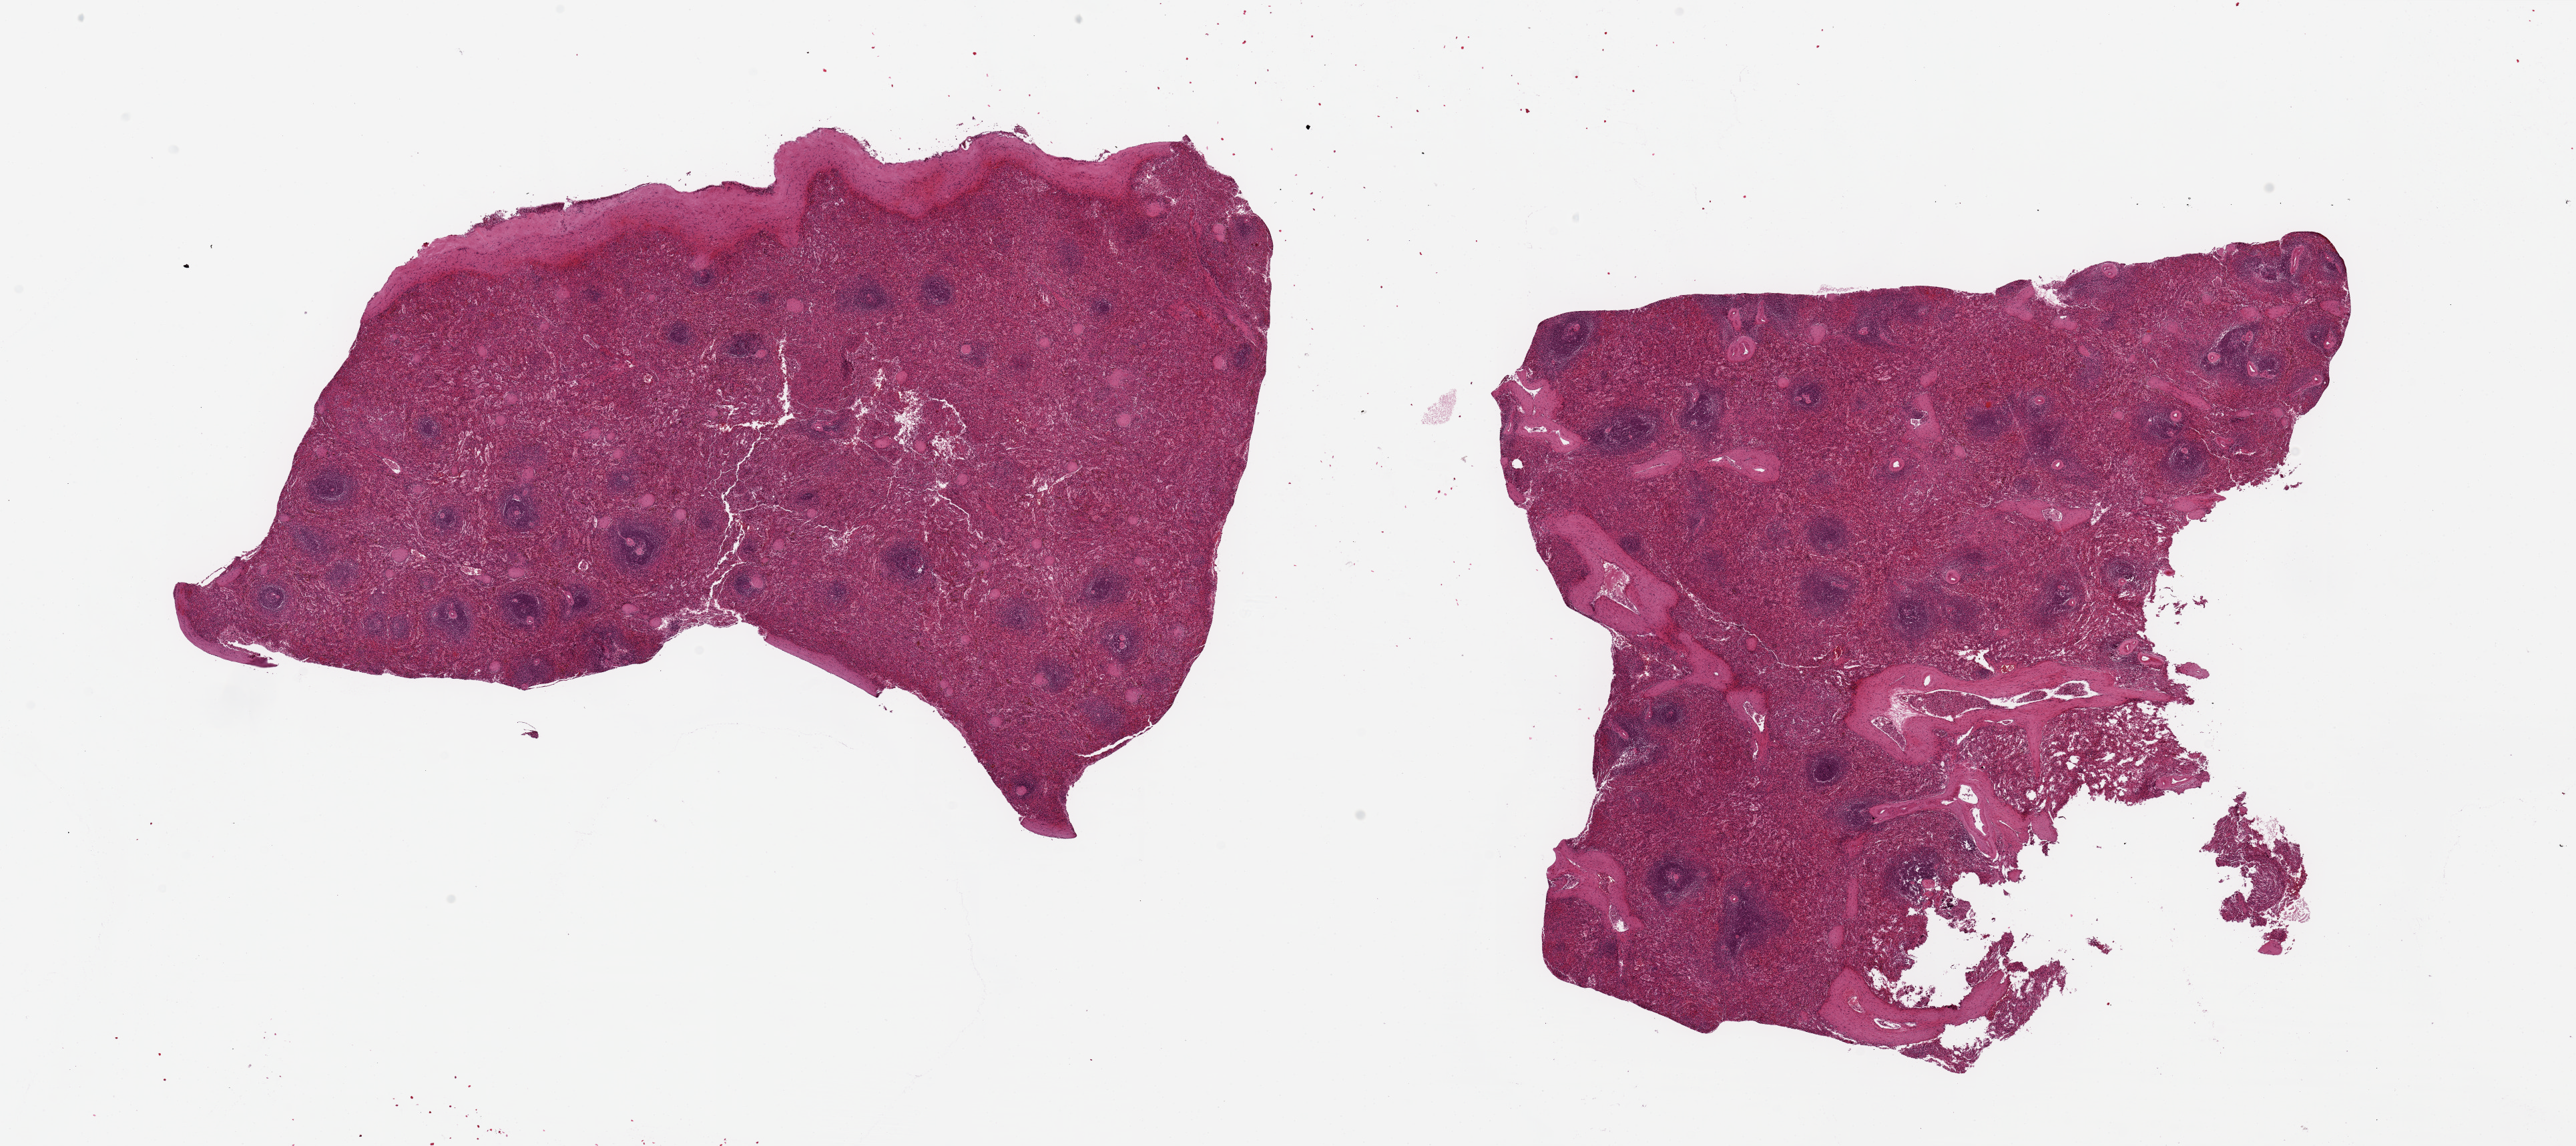
Haematoxylin and eosin whole-slide image, shown as a low-resolution overview of the whole scanned area (about 30.5 x 13.6 mm); PAXgene-fixed paraffin-embedded (PFPE) section; section of spleen (target tissue); donor tissue sample. Female donor.
Pathologist's review note for this sample: 2 pieces, 13x8.5 & 11x10mm; moderately congested; capsule present.